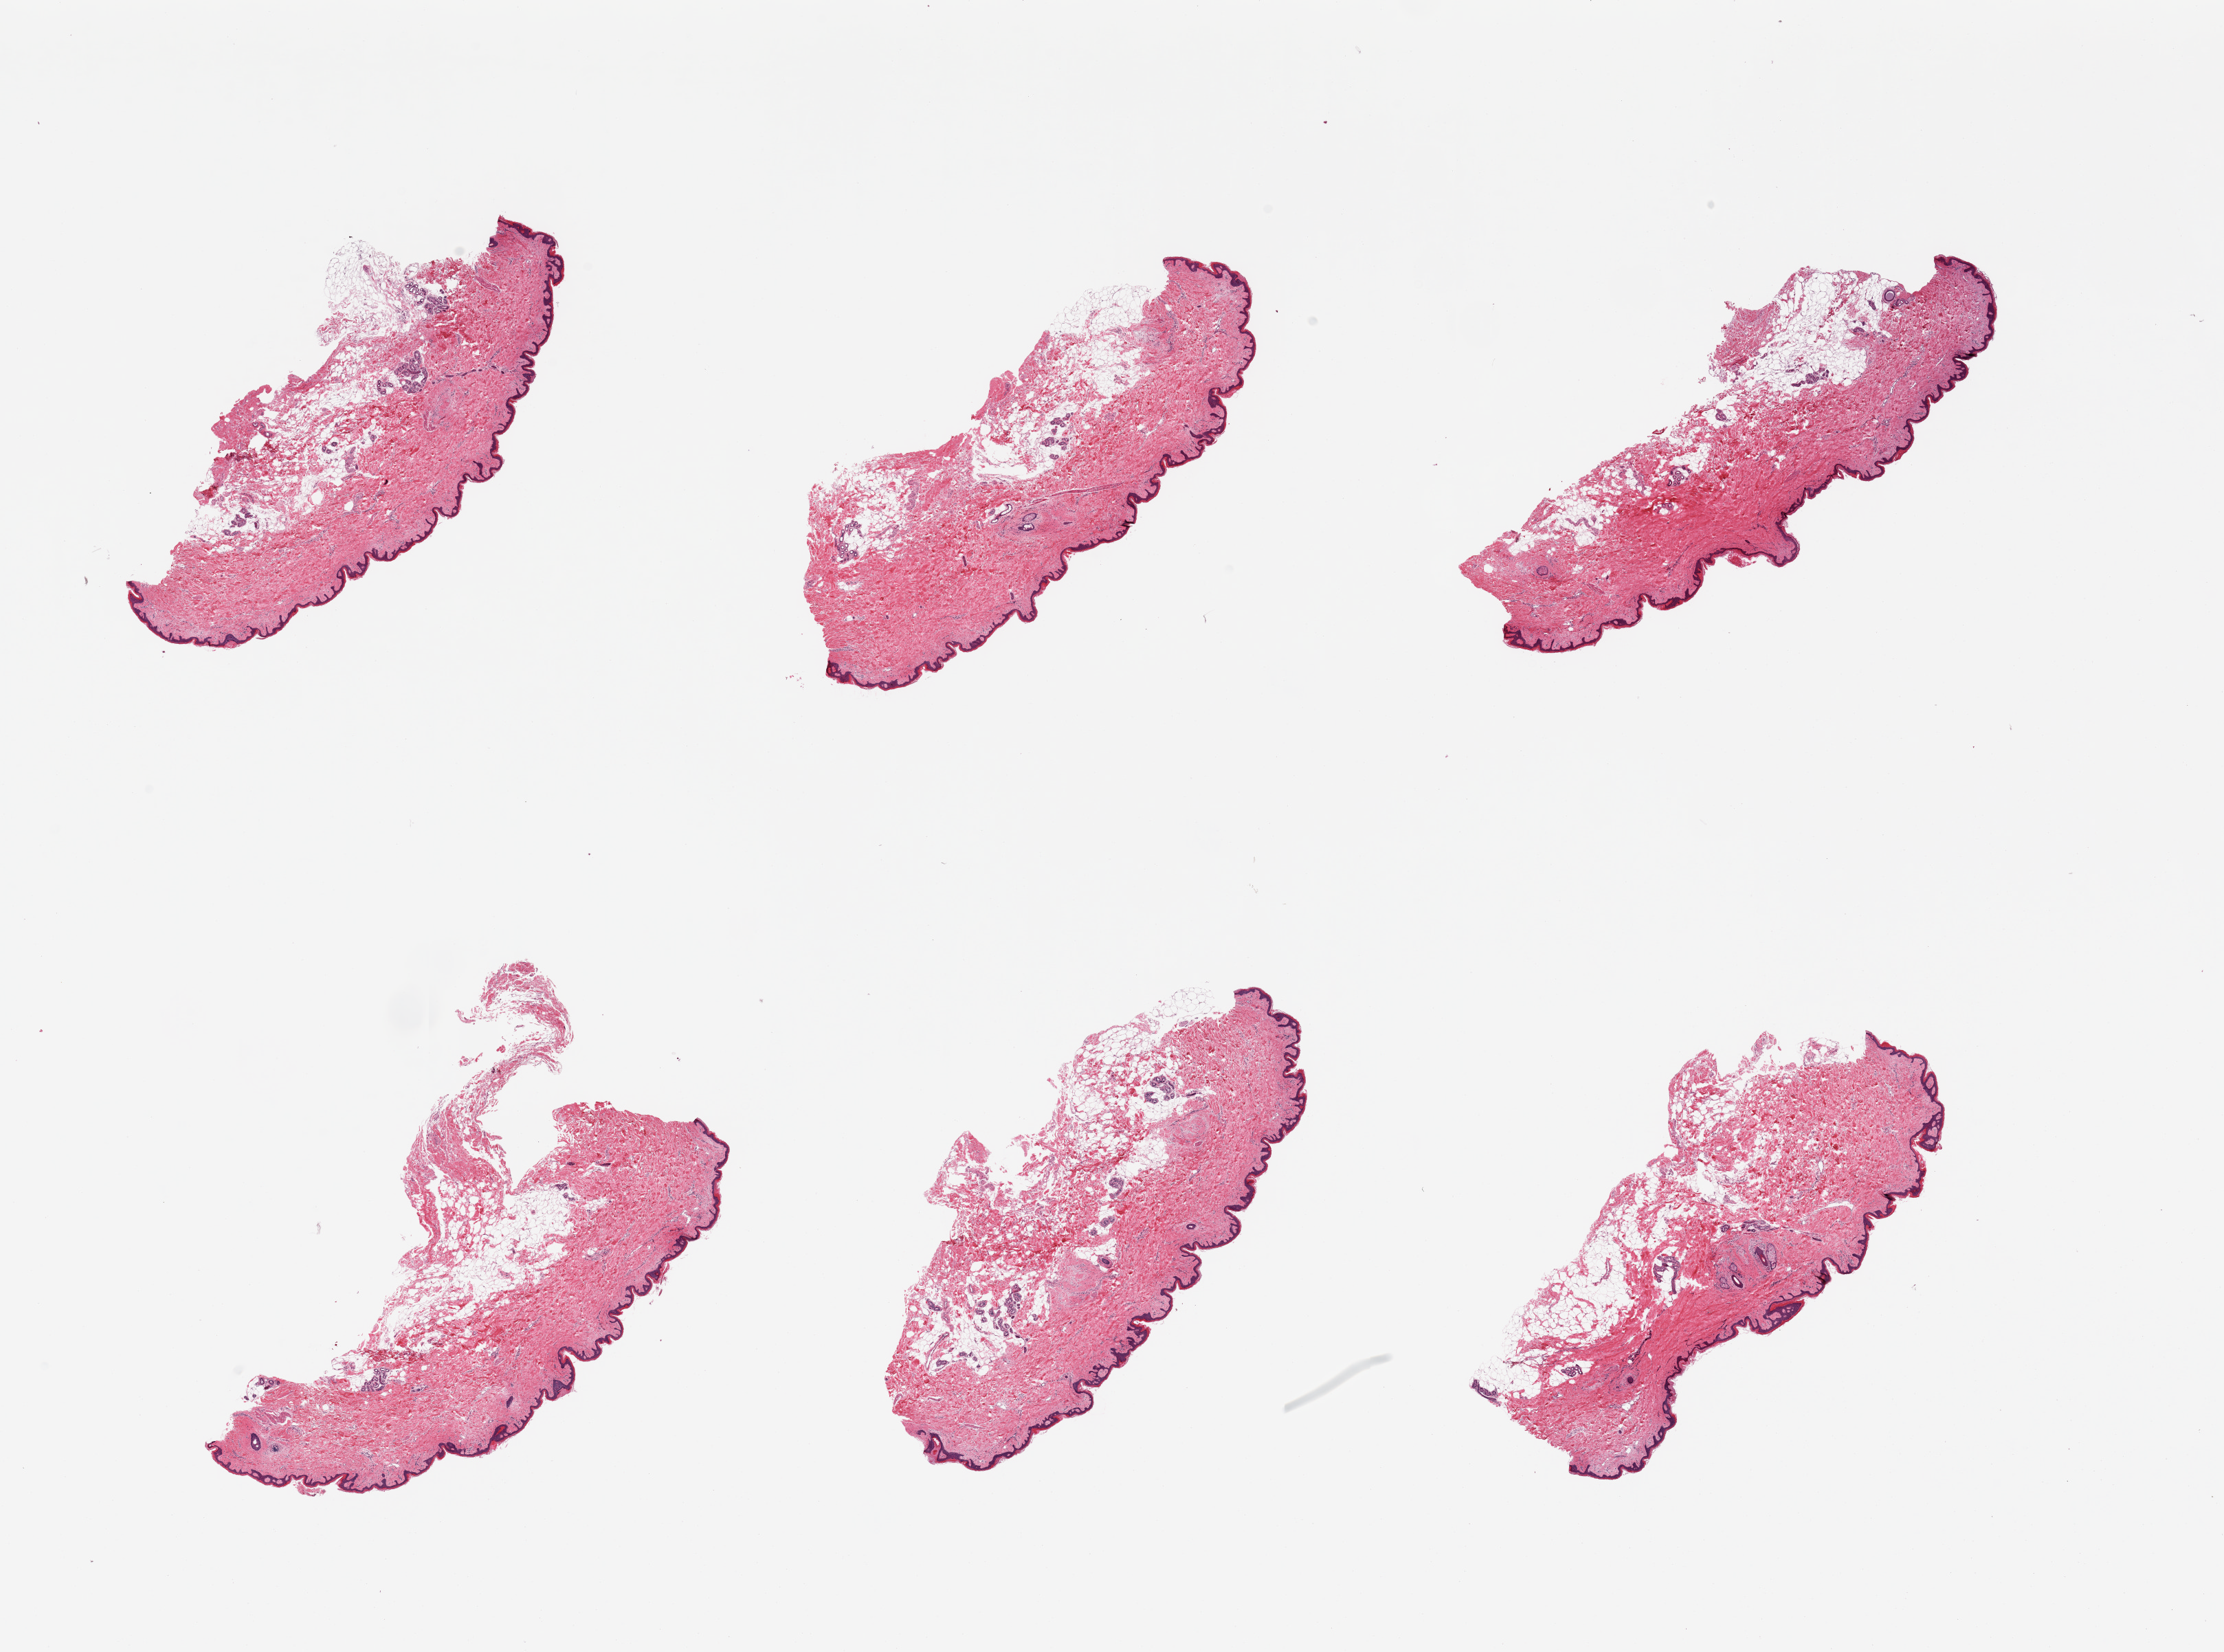
Whole-slide image, H&E stain, whole scanned area (about 25.6 x 19.0 mm, slide scanned at 20x) shown as a low-resolution overview; PAXgene-fixed, paraffin-embedded tissue; section of skin of suprapubic region (target tissue); donor tissue sample. Female donor.
Pathologist's review note for this sample: 6 pieces, up to 15% attached and internal fat.